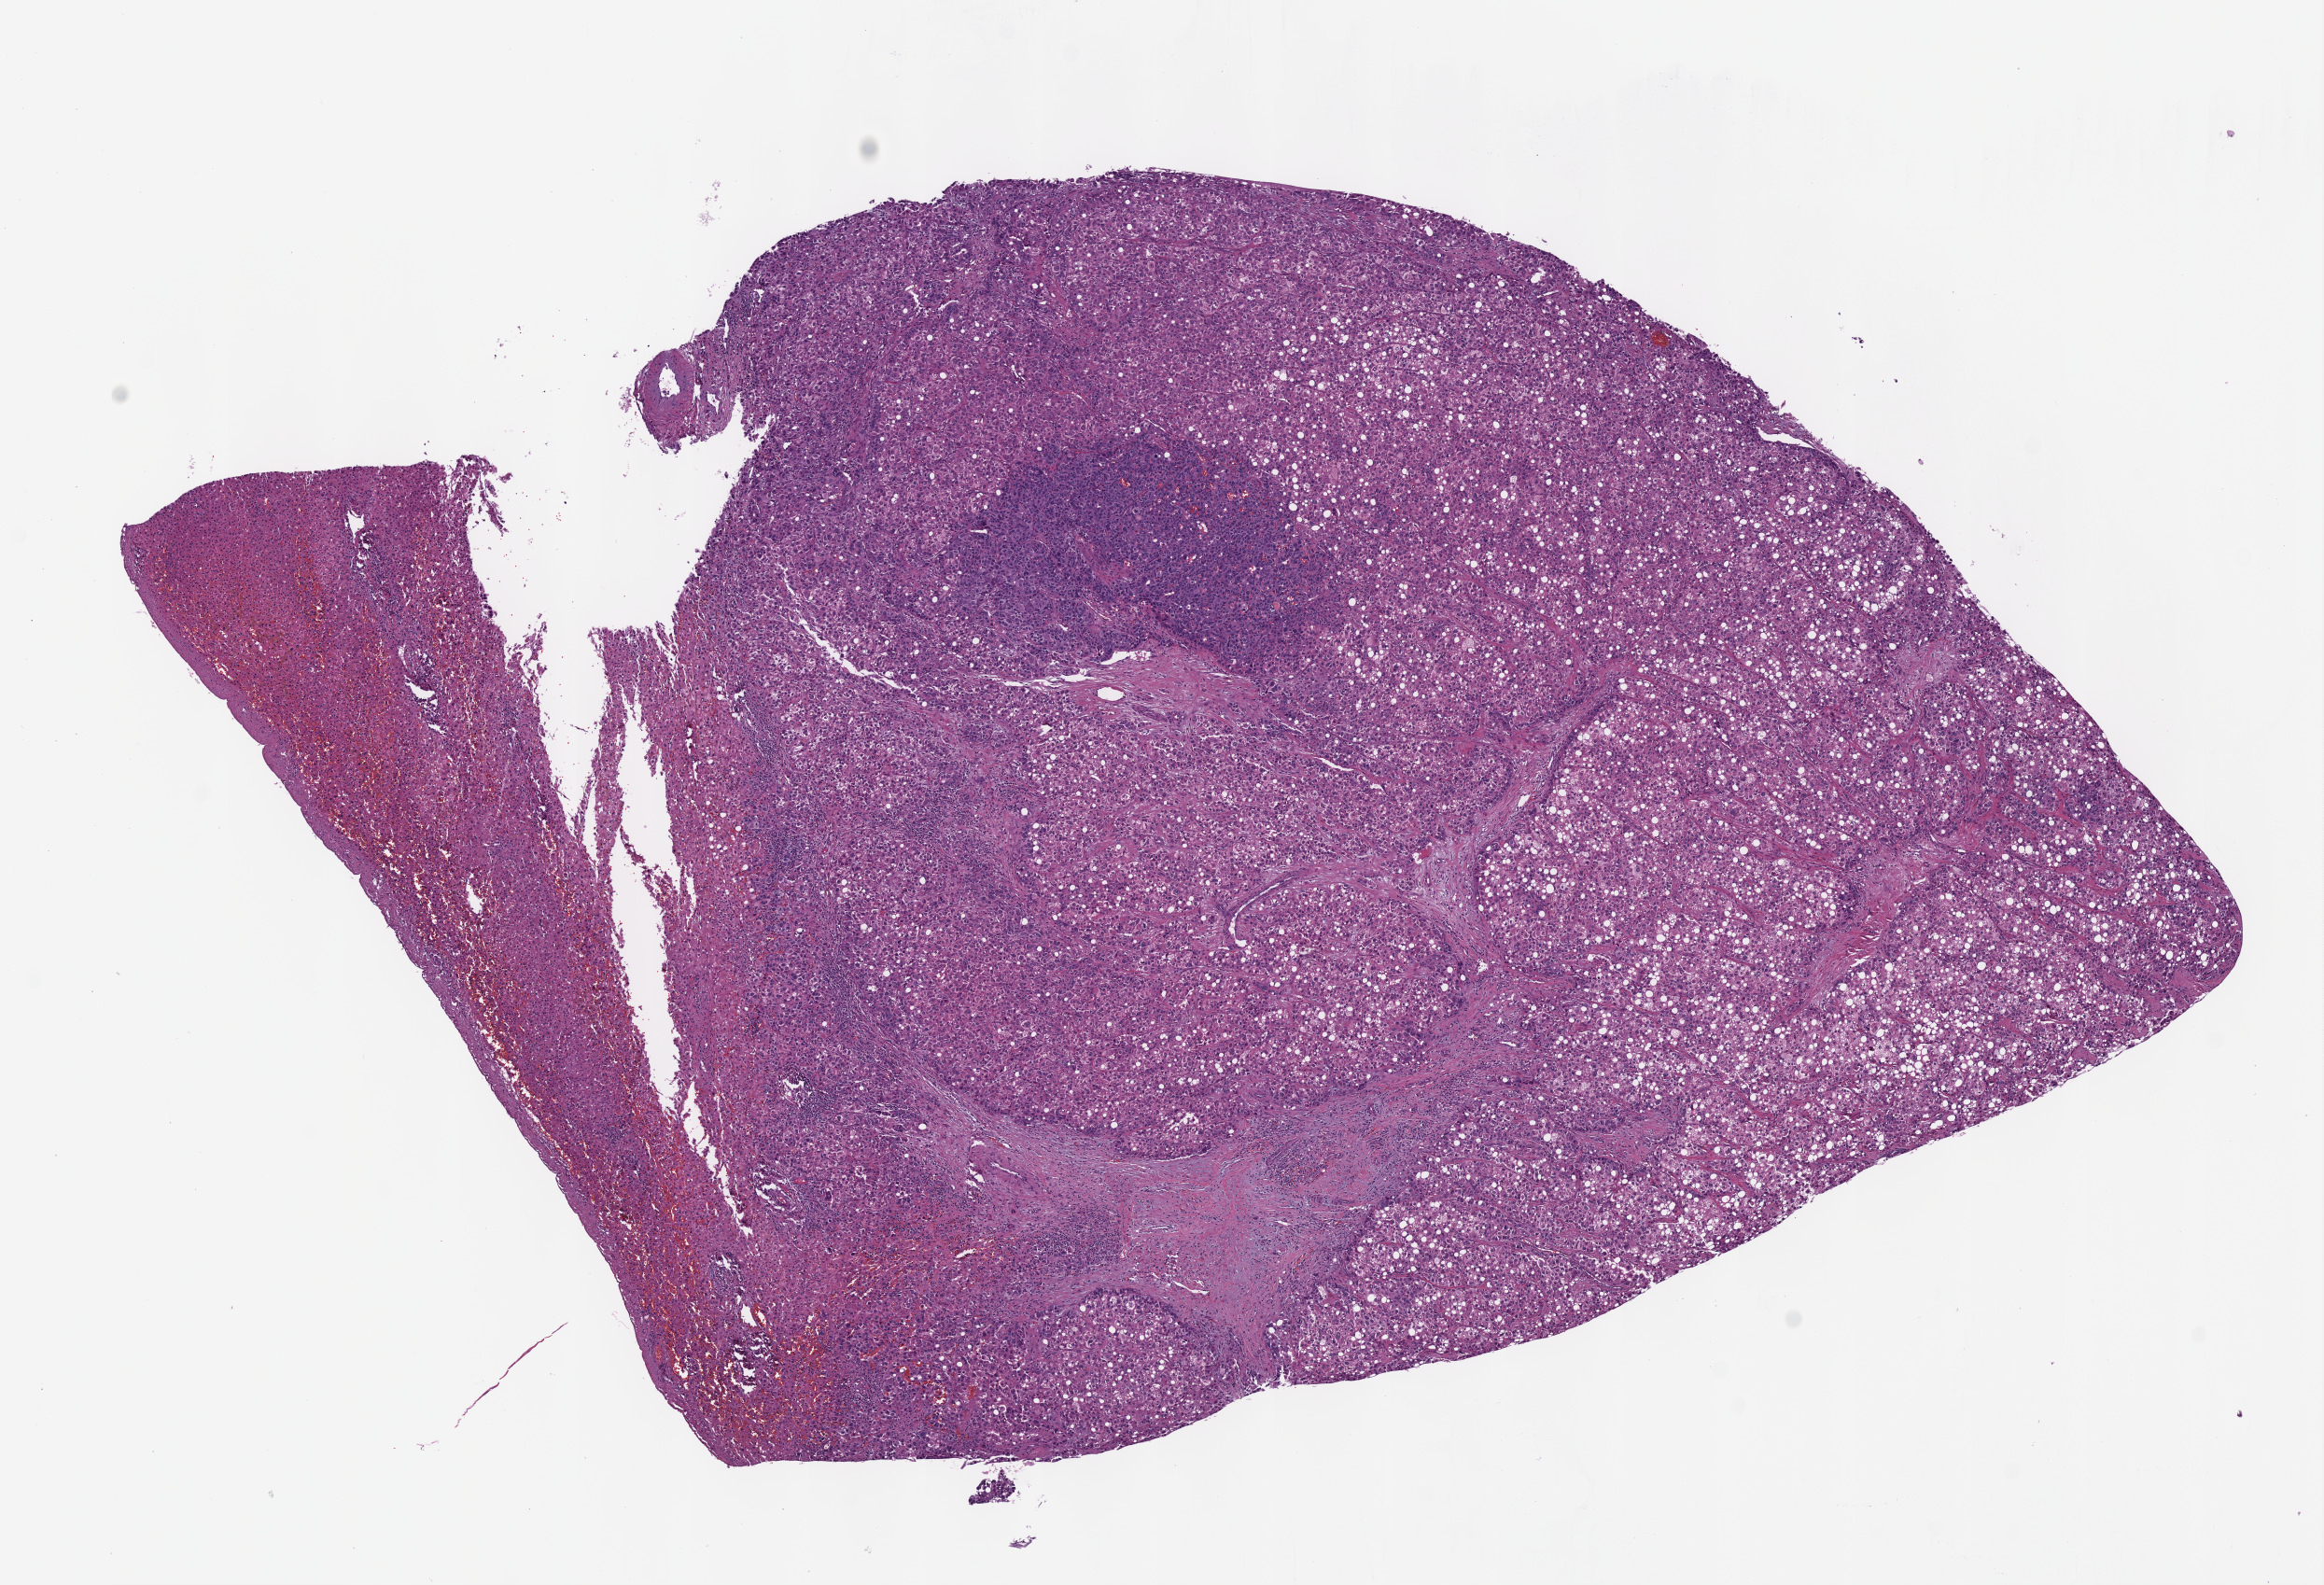
Digitized H&E tissue section (whole slide), shown as a low-resolution overview of the whole scanned area (about 9.8 x 6.7 mm), formalin-fixed paraffin-embedded (FFPE) diagnostic section, sample: primary tumour, liver. Female, age 81 years at initial diagnosis. Histologic grade: G2 (moderately differentiated).
AJCC pathologic stage: II (7th edition). Histologic diagnosis: Hepatocellular carcinoma, NOS. TNM: T2 N0 MX.